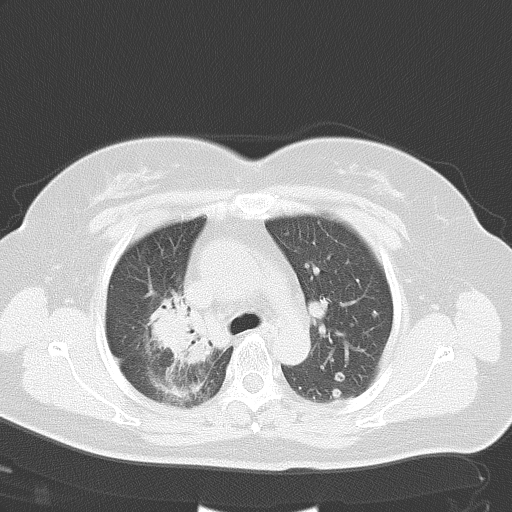
Chest CT, one axial slice. Slice 35 of 48 in the series (ordered by position). Reconstruction kernel B70f. Lung window (W 1500 / L -600 HU). 5 mm slice thickness. 512 × 512 image matrix, field of view 353 × 353 mm. Patient: female, 50 years. Case-level facts recorded for this patient, not image findings: clinical TNM (as recorded): T2a N0 M1a.
Annotated regions visible in this slice (bounding box drawn by a radiologist):
- lung tumour (recorded histology: adenocarcinoma): bounding box [x1, y1, x2, y2] px = [142, 289, 213, 366]